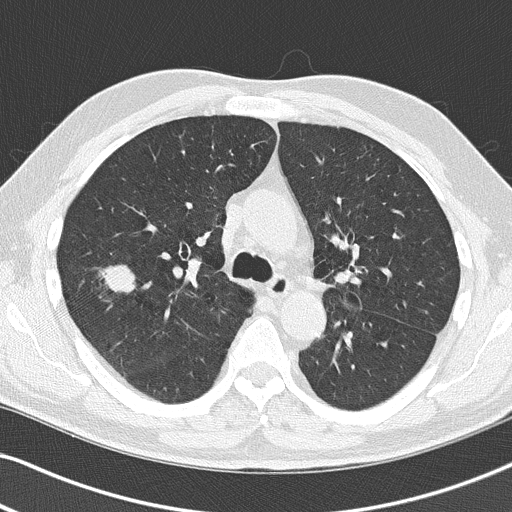
Chest CT (low-dose screening protocol), one axial image; baseline screening round; lung window (W 1500 / L -600 HU); lung (sharp) reconstruction kernel (B50f); 120 kVp. Male participant, aged 67 years at enrolment. Former smoker at enrolment.
- Expert-annotated lung lesion, bounding box [x1, y1, x2, y2] px = [74, 255, 150, 315].
- The exam's reader record, not a measurement of the box and not confirmed to be the same lesion: non-calcified nodule or mass ≥4 mm, right upper lobe, 26 × 24 mm, spiculated (stellate) margins, soft tissue attenuation.
- Official screen result: positive, change unspecified: nodule(s) >= 4 mm or enlarging nodule(s), mass(es), or other non-specific abnormalities suspicious for lung cancer.
- Later outcome: lung cancer diagnosed 49 days after this screen — squamous cell carcinoma, NOS, right upper lobe, poorly differentiated (G3), stage IA (AJCC 6th edition), 27 mm at pathology.